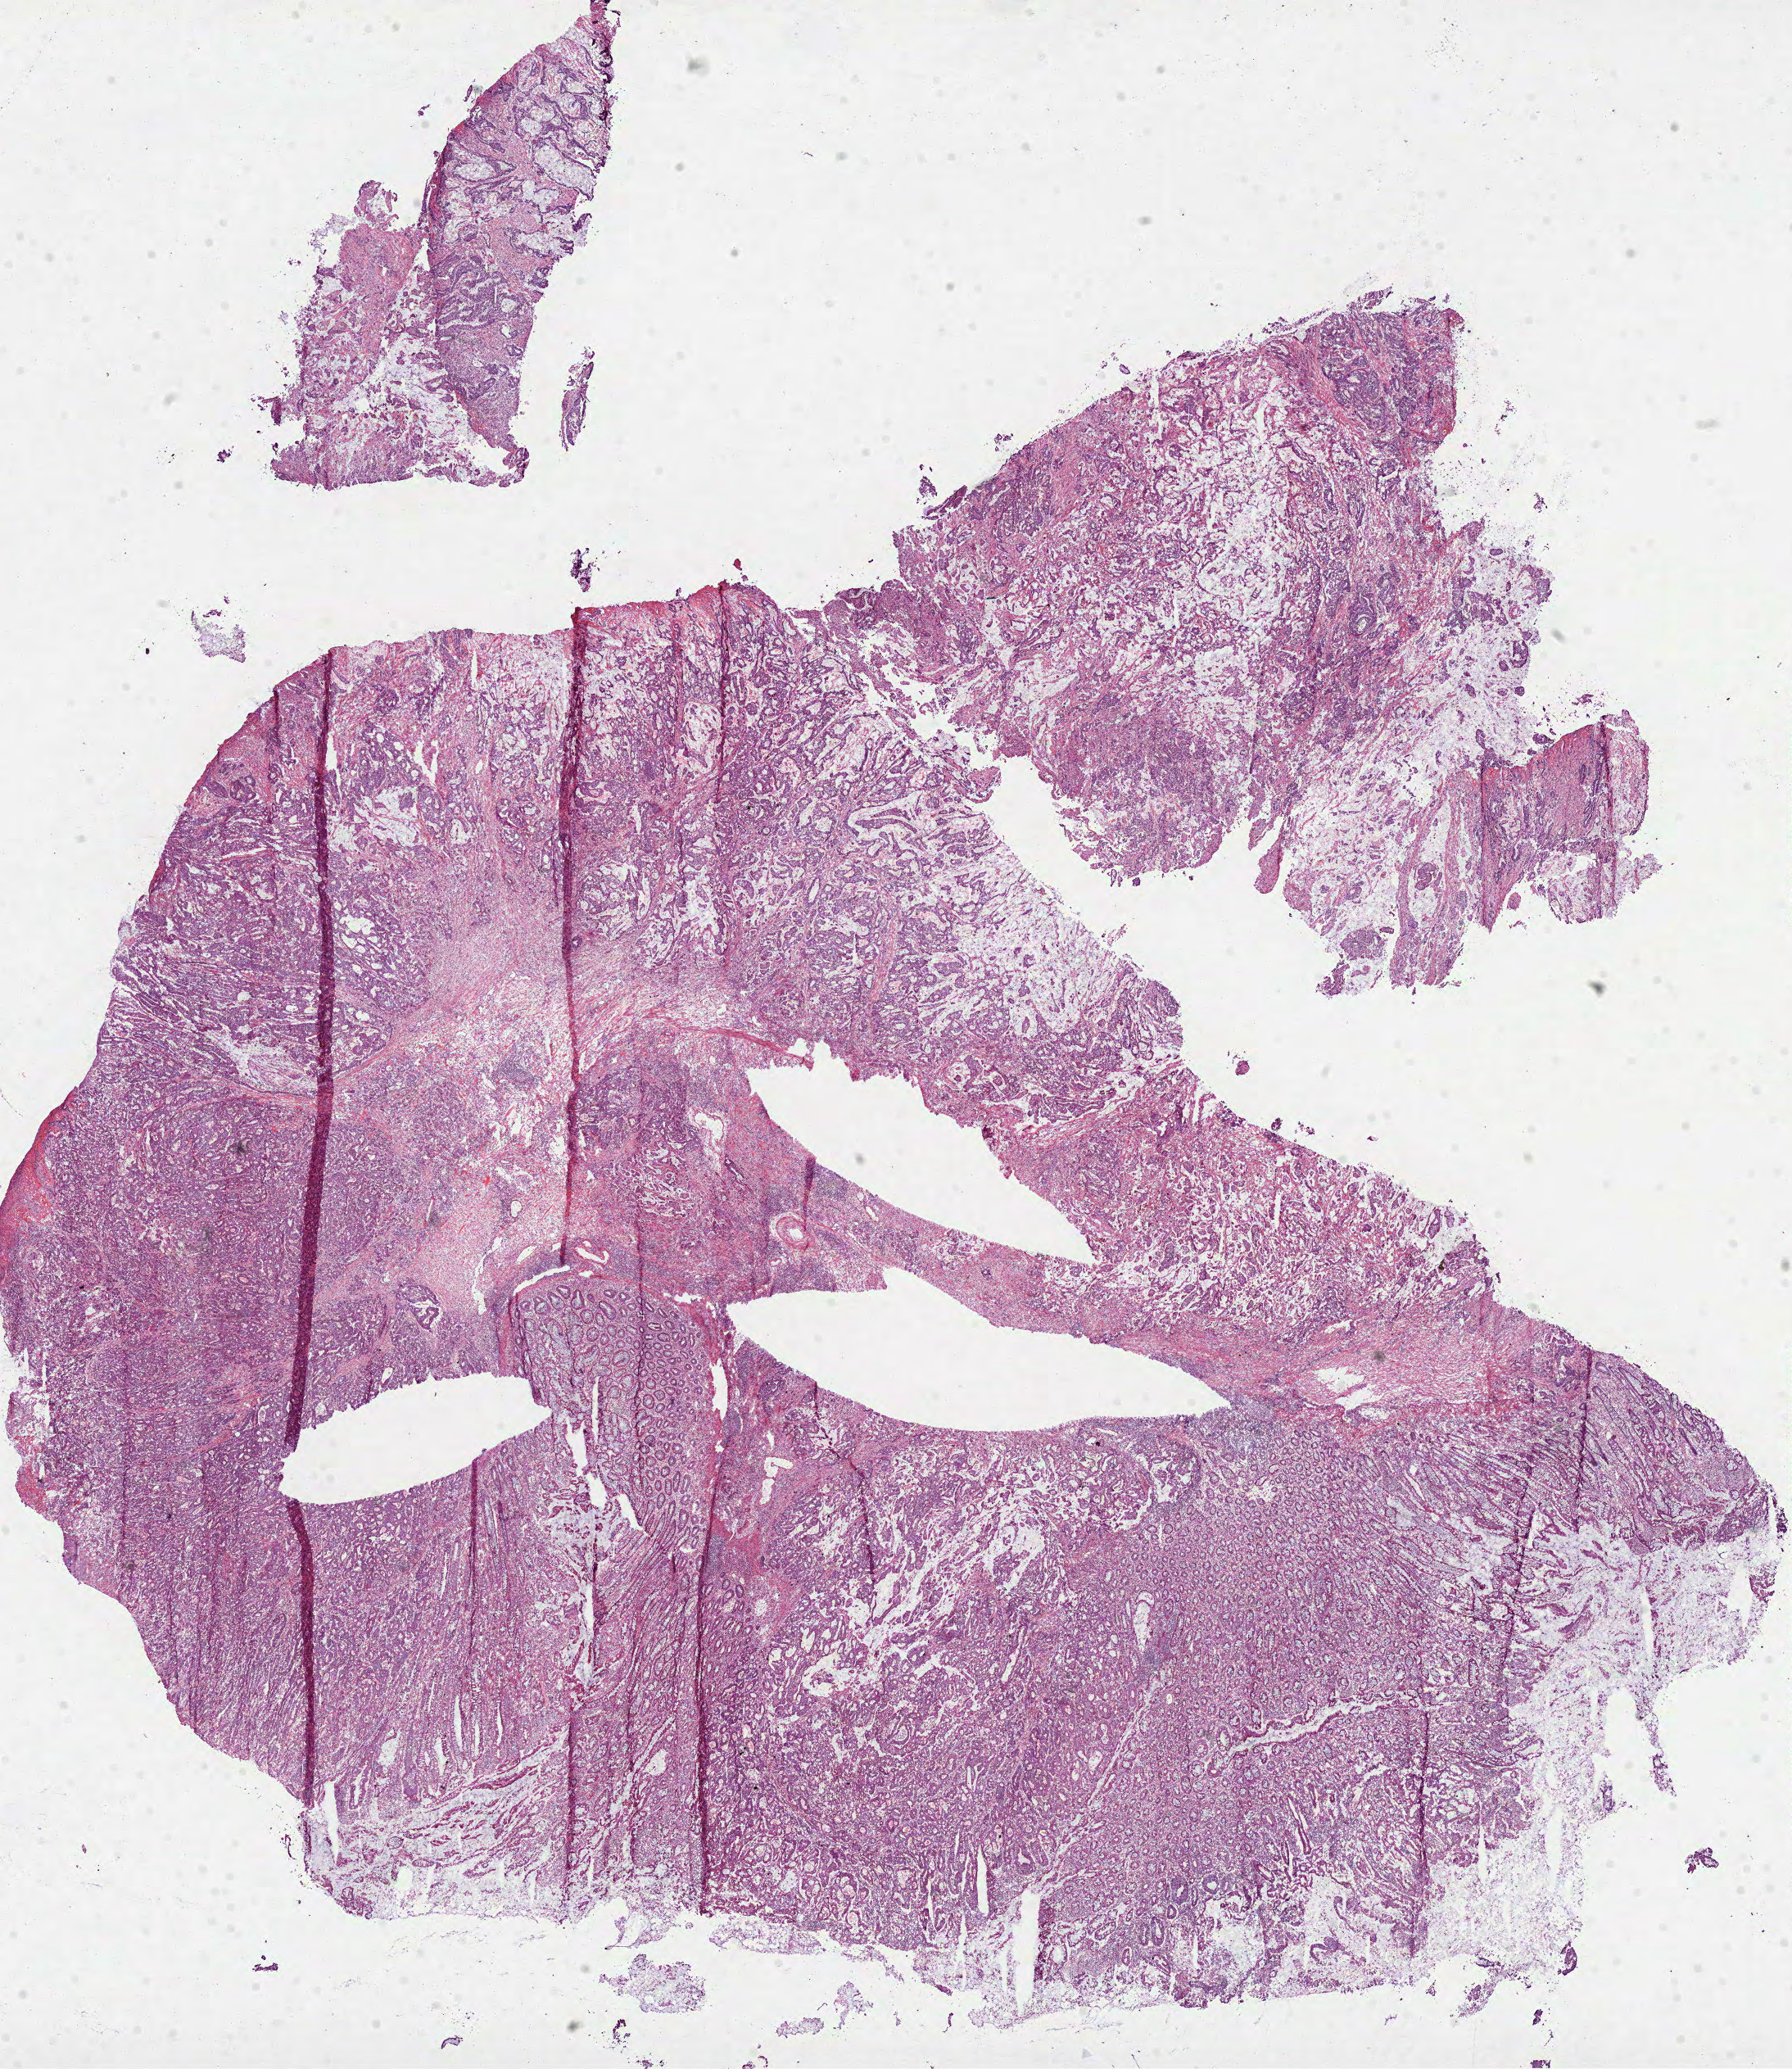
H&E-stained whole-slide image — a low-resolution overview of the entire scanned area, about 17.6 x 20.4 mm; frozen section from the bottom of the tissue portion; colon, primary tumour sample. Patient: male, age at initial diagnosis 64 years. Composition of this section per pathologist review: tumour cells 60%, tumour nuclei 75%, normal cells 15%, stromal cells 20%, necrosis 5%.
* AJCC pathologic stage: IV
* TNM: T4 N1 M1
* histologic diagnosis: Adenocarcinoma, NOS (ascending colon)